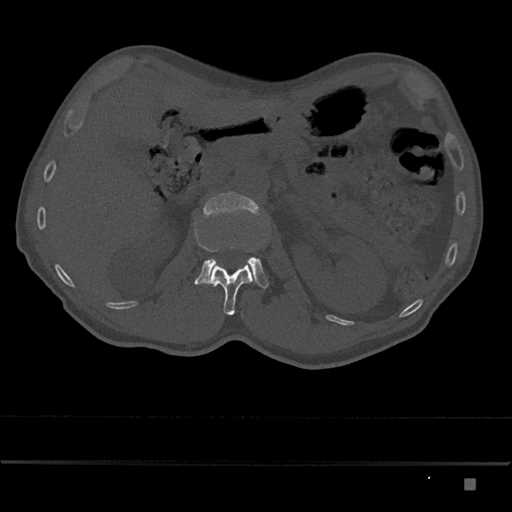
CT including the spine, one axial slice; bone window (W 1800 / L 400 HU); 0.5 mm slice thickness; 512 × 512 image matrix, field of view 390 × 390 mm. Patient: male, 72 years. Case-level facts recorded for this patient, not image findings: primary cancer: prostate.
Structures marked on this image (semi-automatic segmentation, software-assisted and operator-edited):
- L1 vertebra: bounding box (x1, y1, x2, y2) in pixels: (208, 260, 254, 315)
- L2 vertebra: (194, 192, 269, 289)